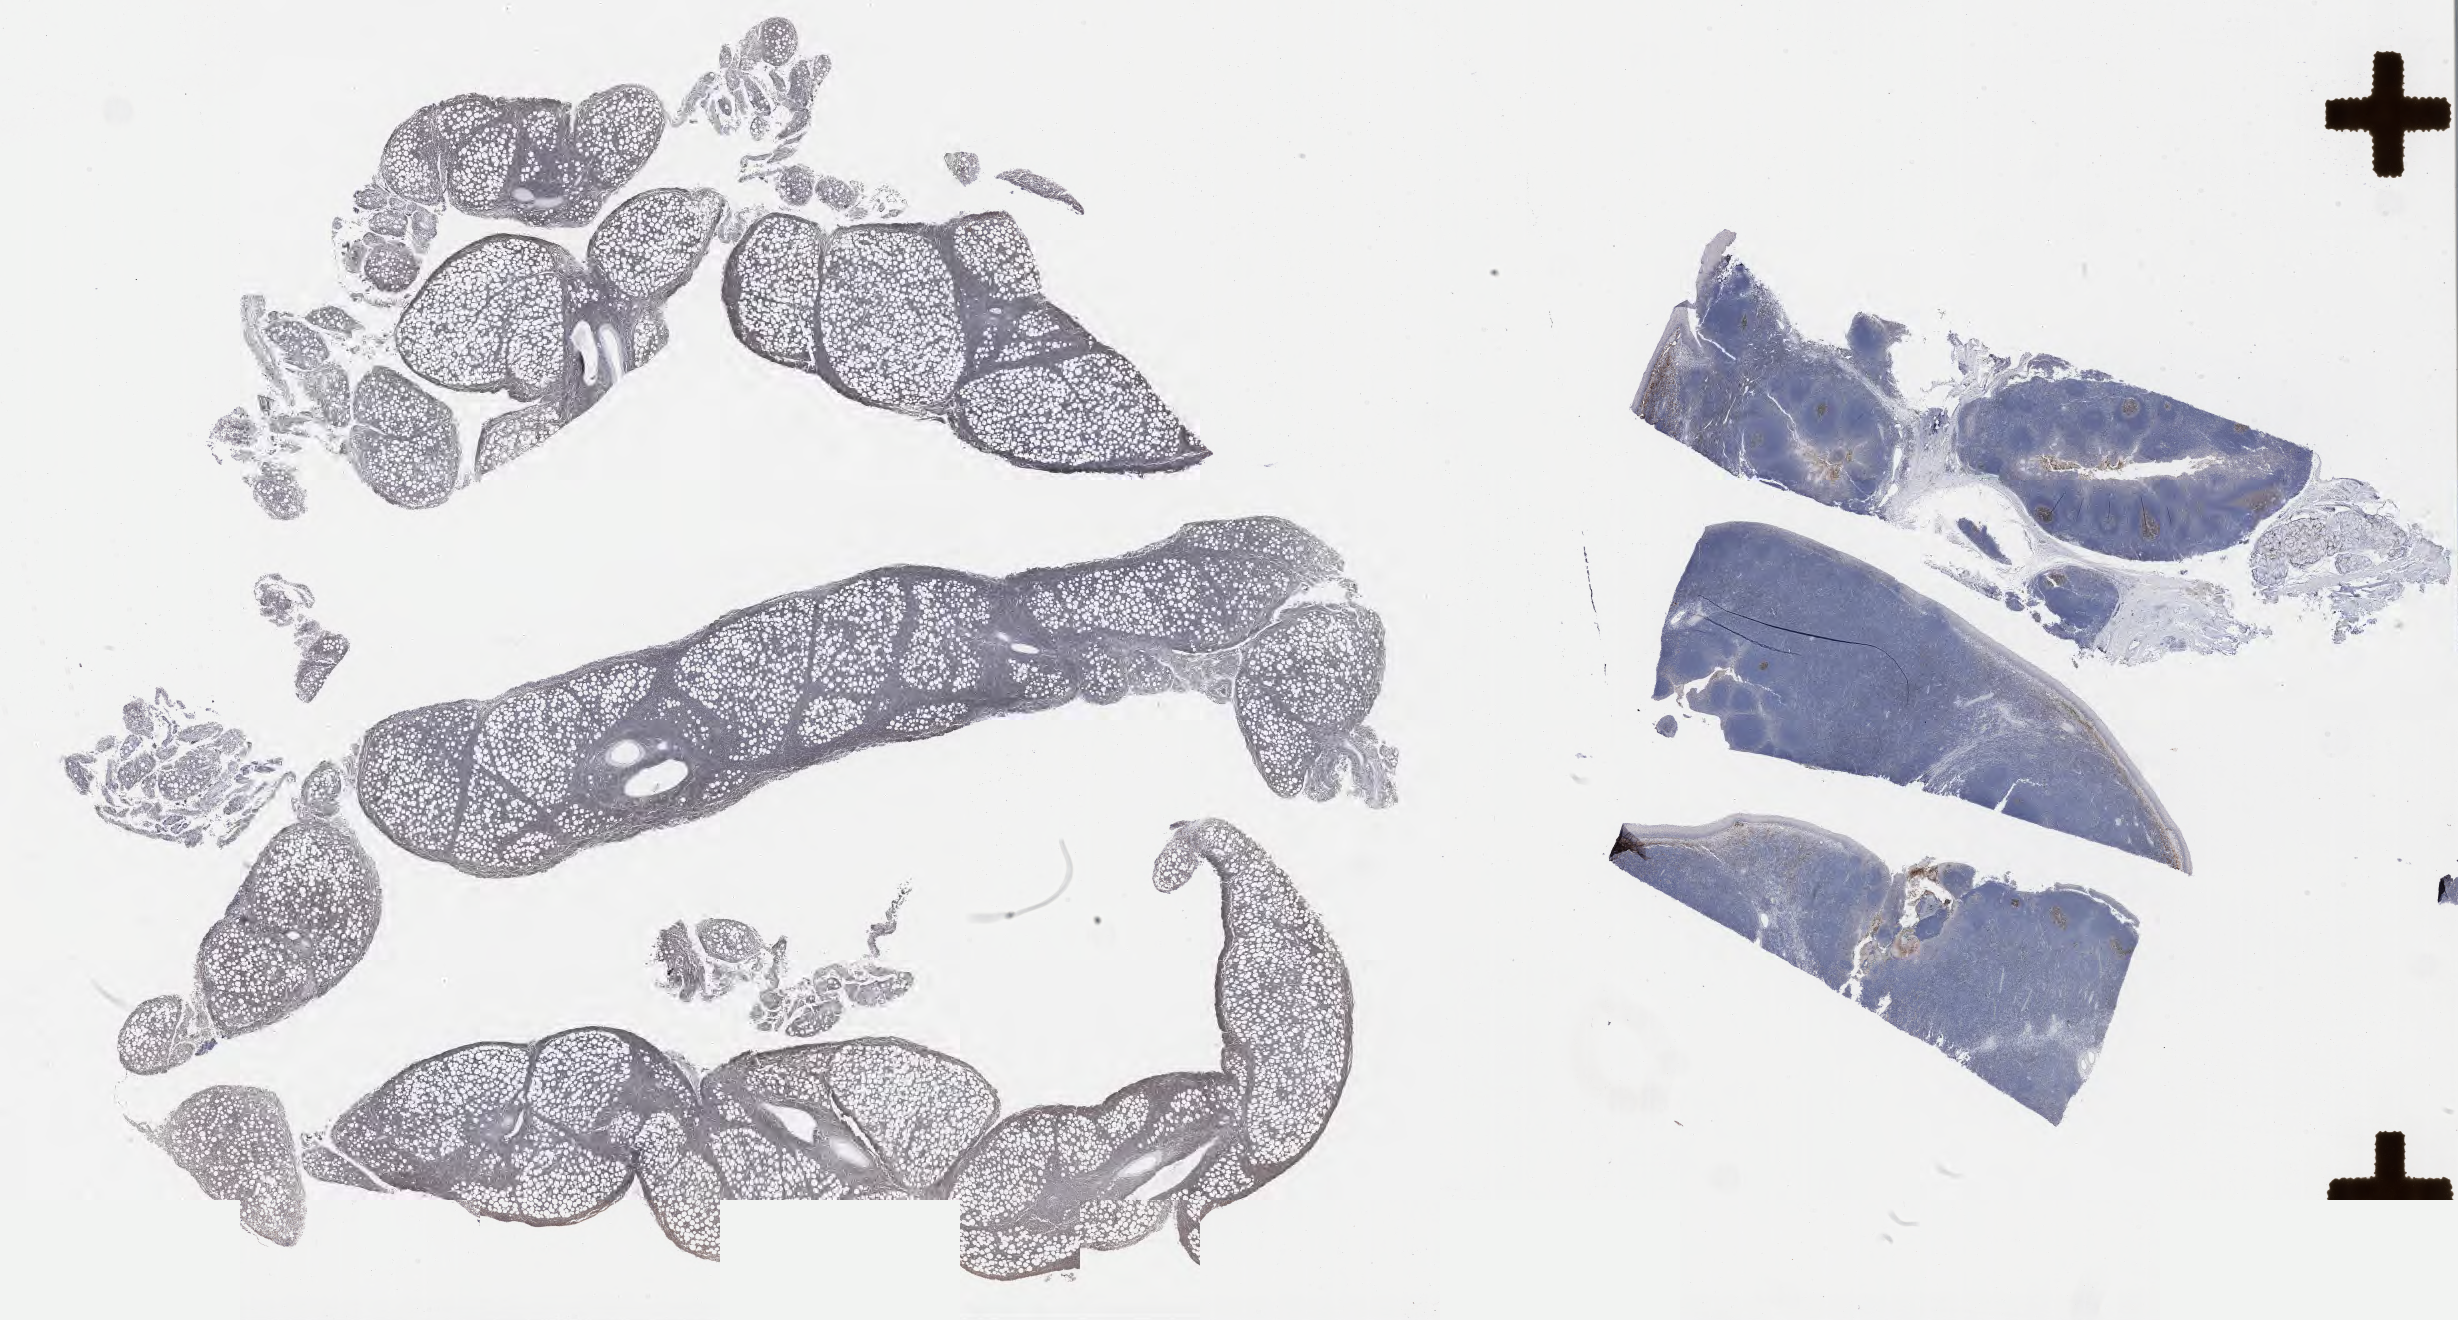
Whole-slide image, immunohistochemical stain for CD10, shown as a low-resolution overview of the whole scanned area (about 39.8 x 21.4 mm); tumor tissue; anatomic site: abdomen proper. Female patient; age at initial diagnosis 9 years.
Histologic diagnosis: Burkitt lymphoma, NOS.